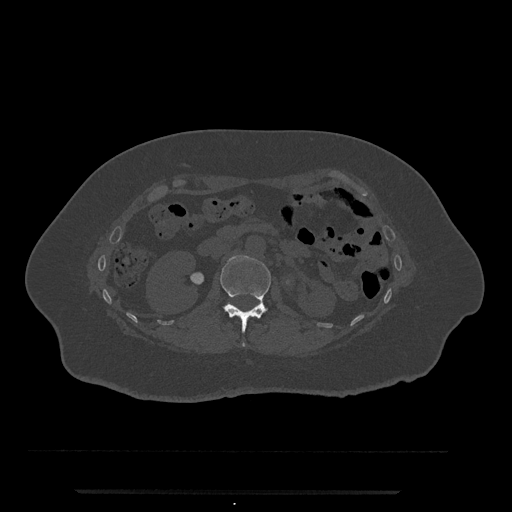
CT including the spine, one axial slice. Slice 98 of 797 in the series (ordered by position). 120 kVp. Bone window (W 1800 / L 400 HU). 0.5 mm slice thickness. 512 × 512 image matrix. Patient: female, 51 years. Case-level facts recorded for this patient, not image findings: primary cancer: neuro; vertebrae with lytic lesions (as recorded): T8.
Structures marked on this image (semi-automatic segmentation, software-assisted and operator-edited):
- L1 vertebra: bounding box [x1, y1, x2, y2] px = [220, 255, 271, 346]